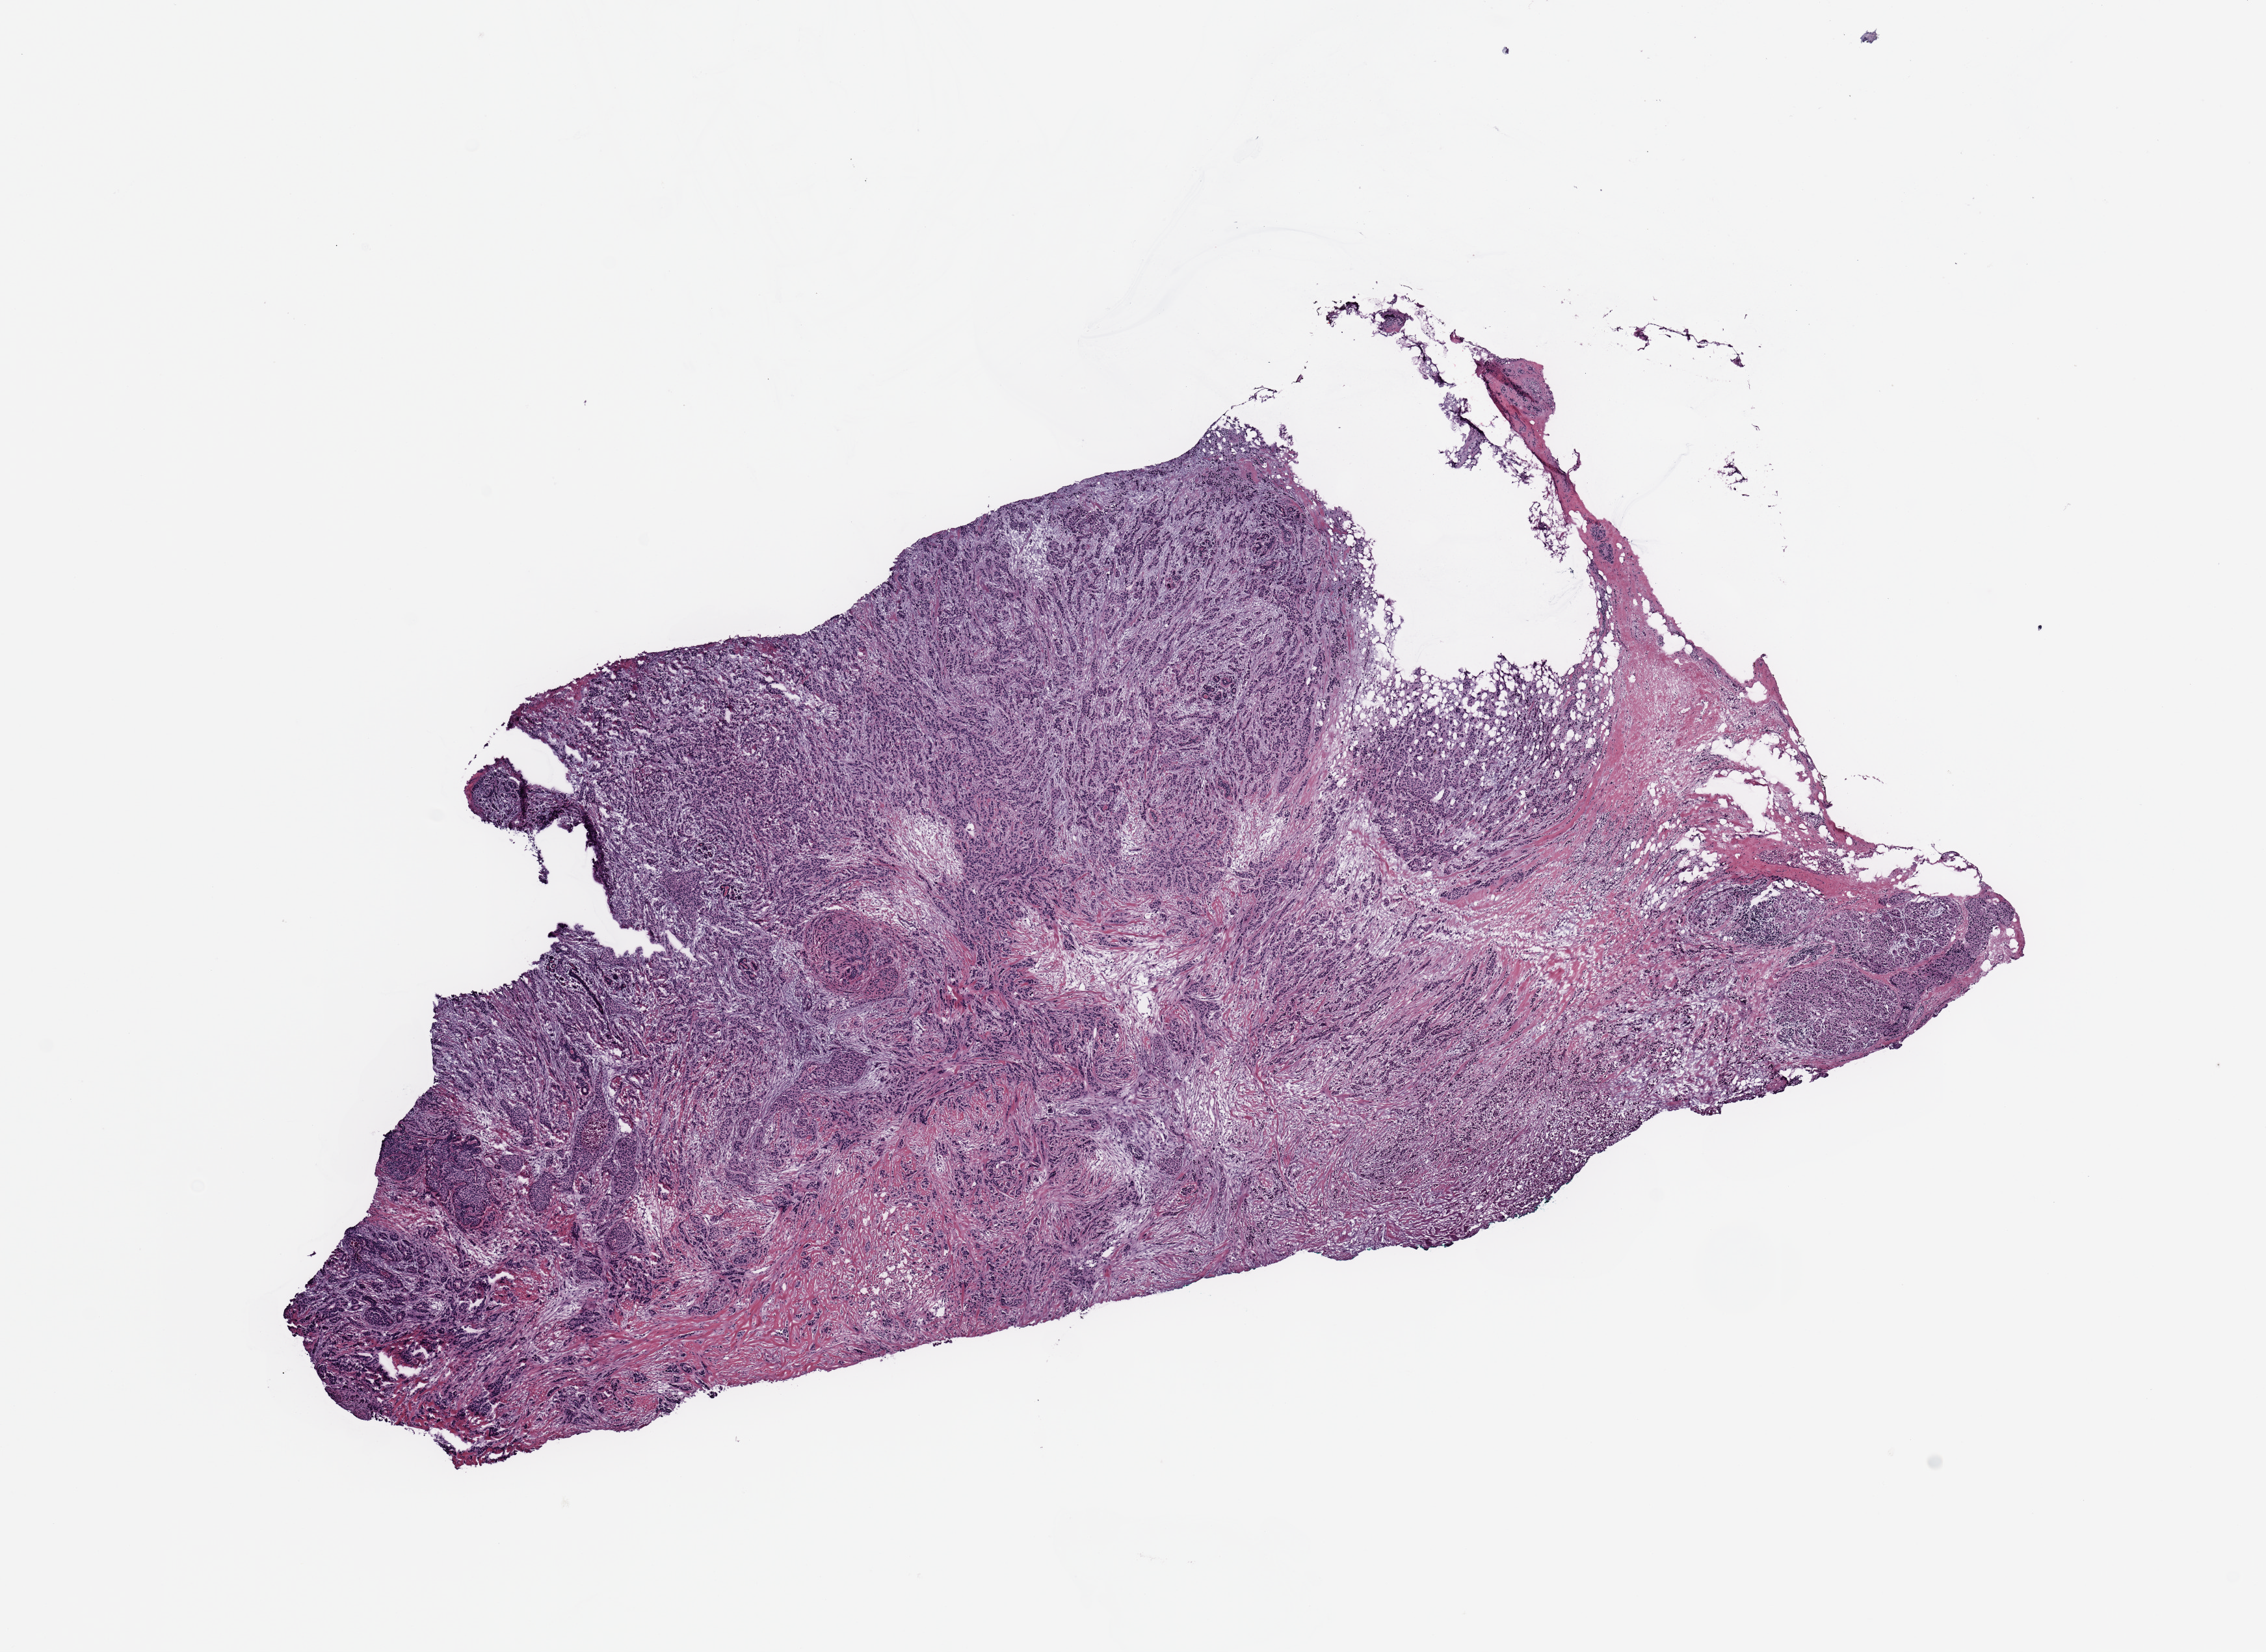
Whole-slide histology image, H&E-stained, shown as a low-resolution overview of the whole scanned area (about 13.8 x 10.0 mm, from a 20x scan). Tumour tissue sample, breast. Female, 52 y/o.
Histologic diagnosis: Infiltrating duct carcinoma, NOS. AJCC pathologic stage: IA.